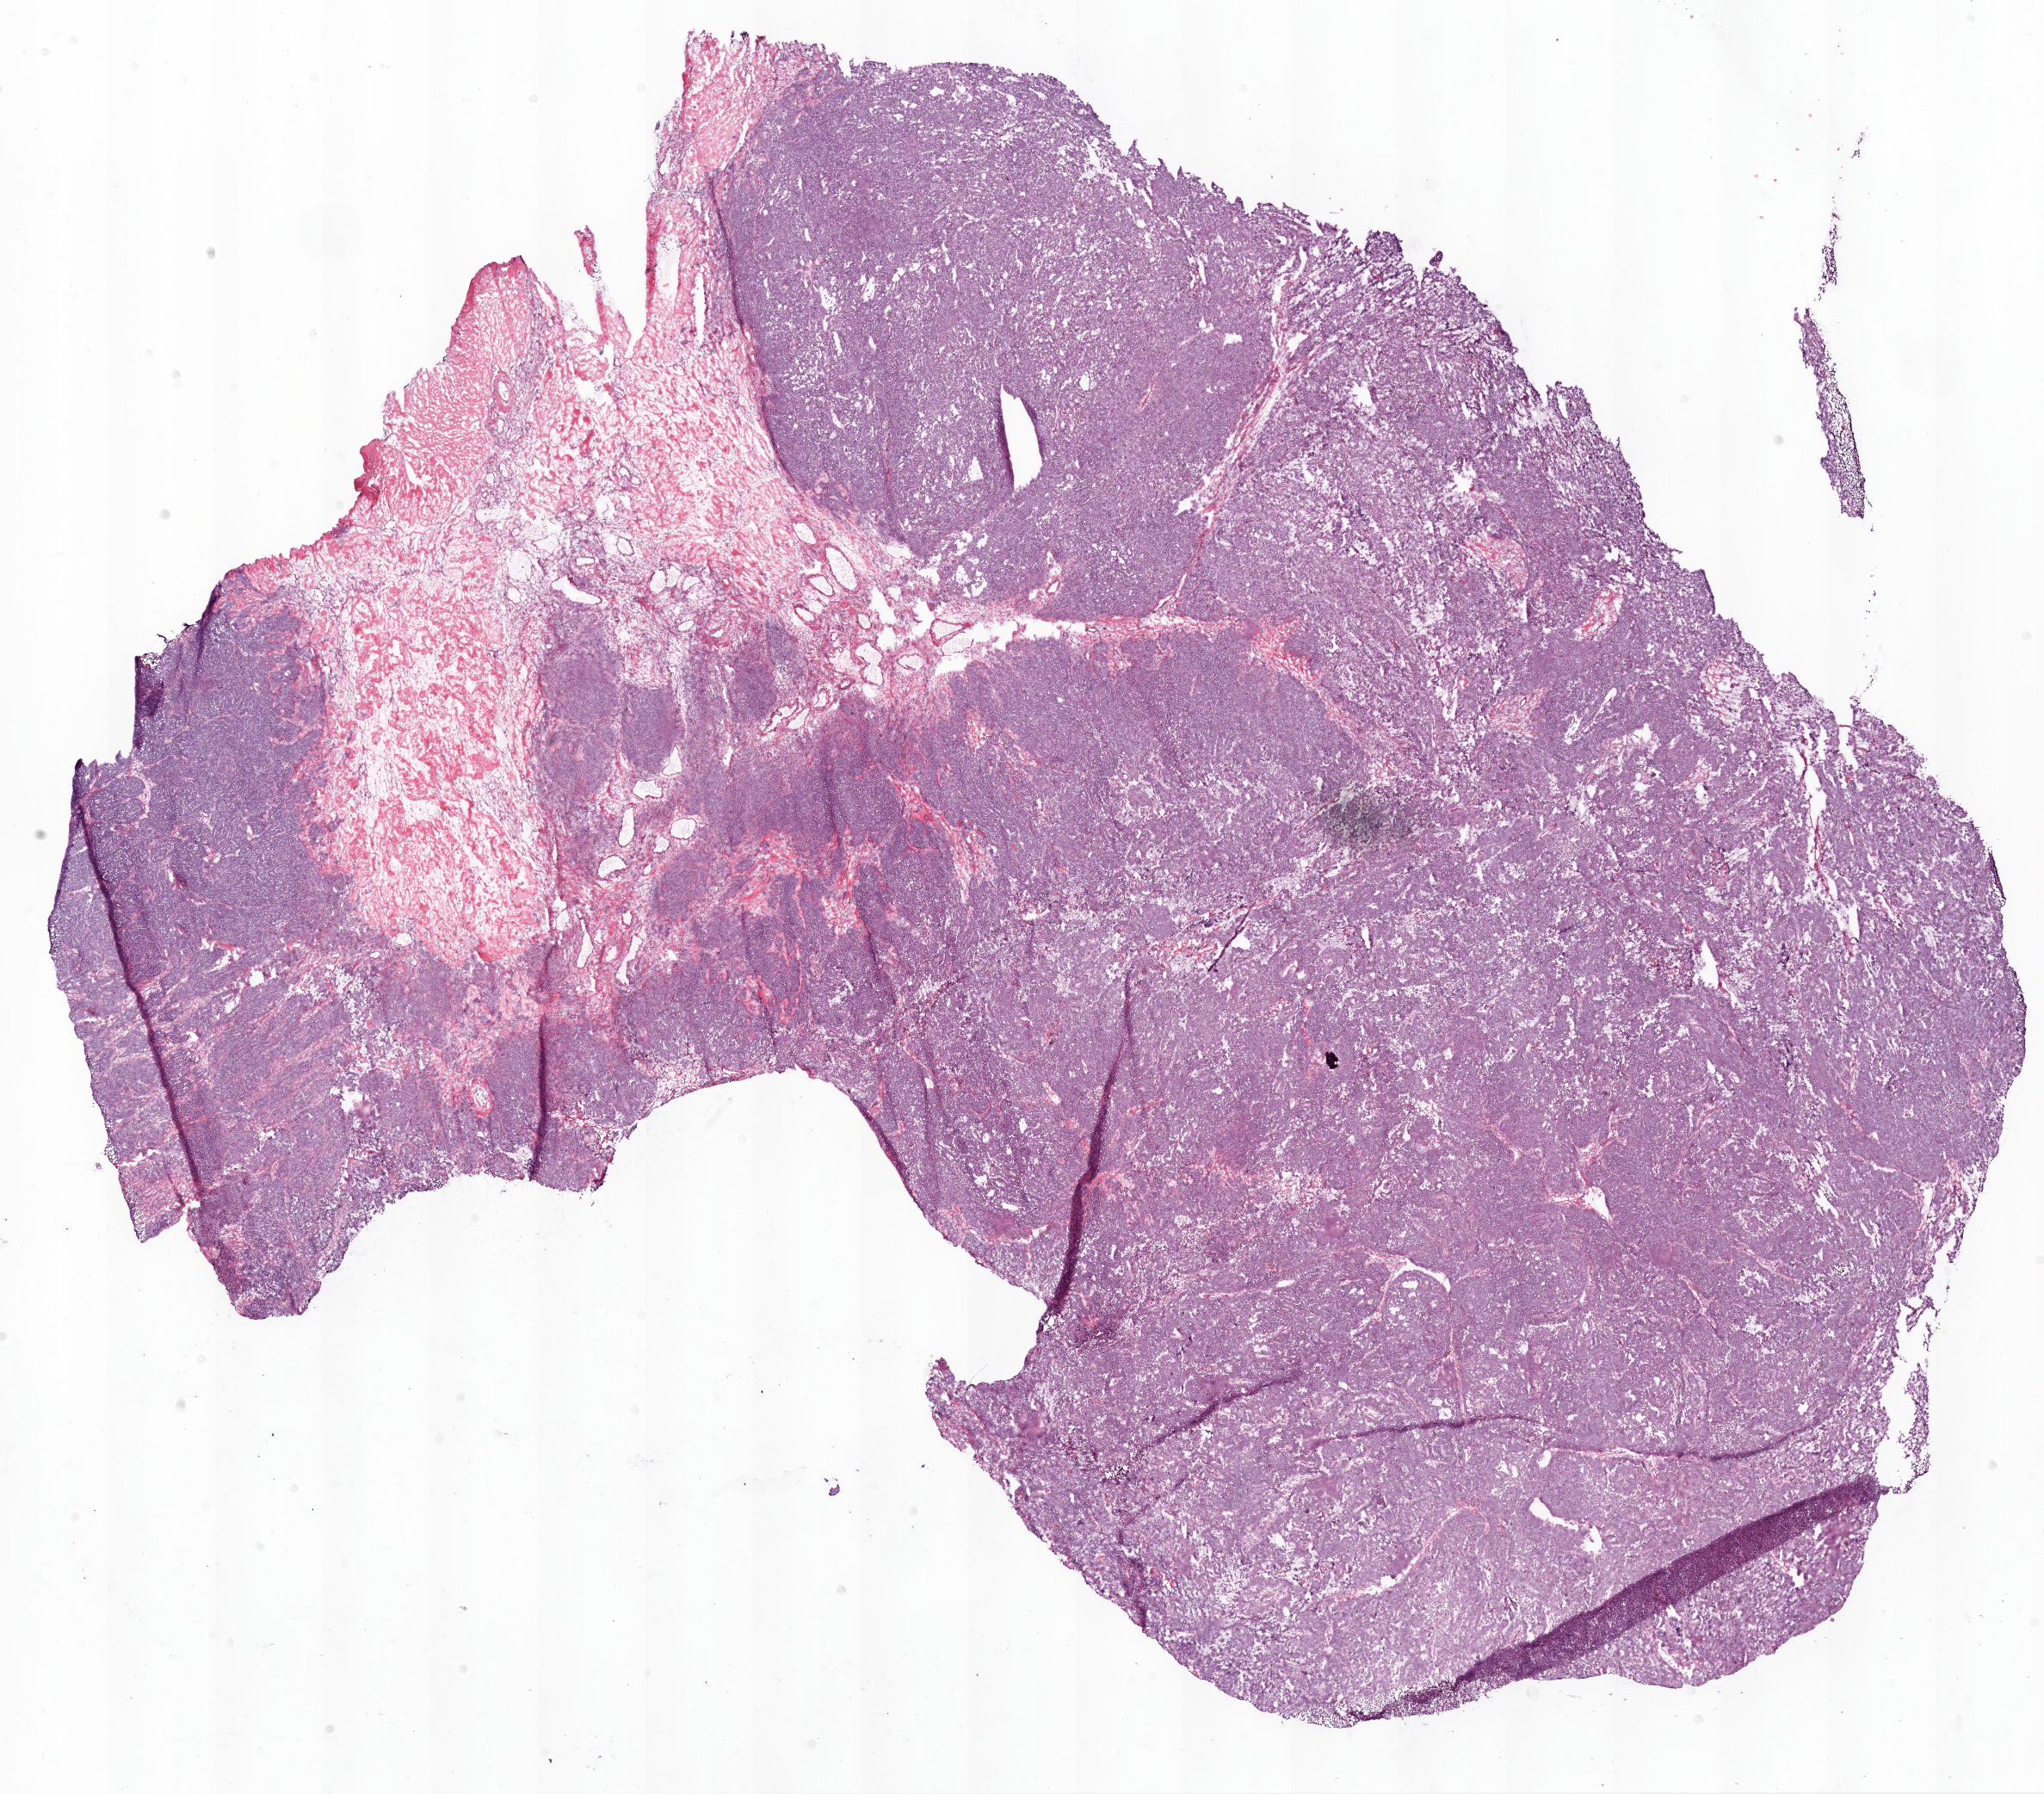
Hematoxylin and eosin (H&E) stained whole-slide image, shown as a low-resolution overview of the whole scanned area (about 19.1 x 16.7 mm, acquisition: 20x scan); frozen section; ovary, primary tumour sample. Patient: female, age at initial diagnosis 76 years. Histologic grade: G3 (poorly differentiated). Composition of this section per pathologist review: tumour cells 85%, tumour nuclei 90%, normal cells 0%, stromal cells 0%, necrosis 15%. Inflammatory infiltration, as recorded: lymphocyte infiltration 3%, monocyte infiltration 2%.
• diagnosis: Serous cystadenocarcinoma, NOS
• FIGO stage: IIIB